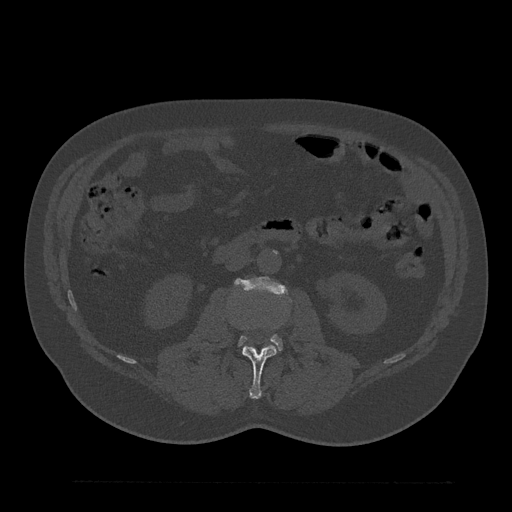
CT including the spine, one axial slice; position 73 of 797 along the scan axis; bone window (W 1800 / L 400 HU); 0.5 mm slice thickness; 512 × 512 image matrix, field of view 430 × 430 mm. Male patient, age 61 years. From the clinical record (not read from this slice): primary cancer: prostate.
Annotated regions visible in this slice (semi-automatically segmented with operator editing):
- L2 vertebra: bounding box (x1, y1, x2, y2) in pixels: (231, 322, 276, 399)
- L3 vertebra: (235, 277, 286, 350)